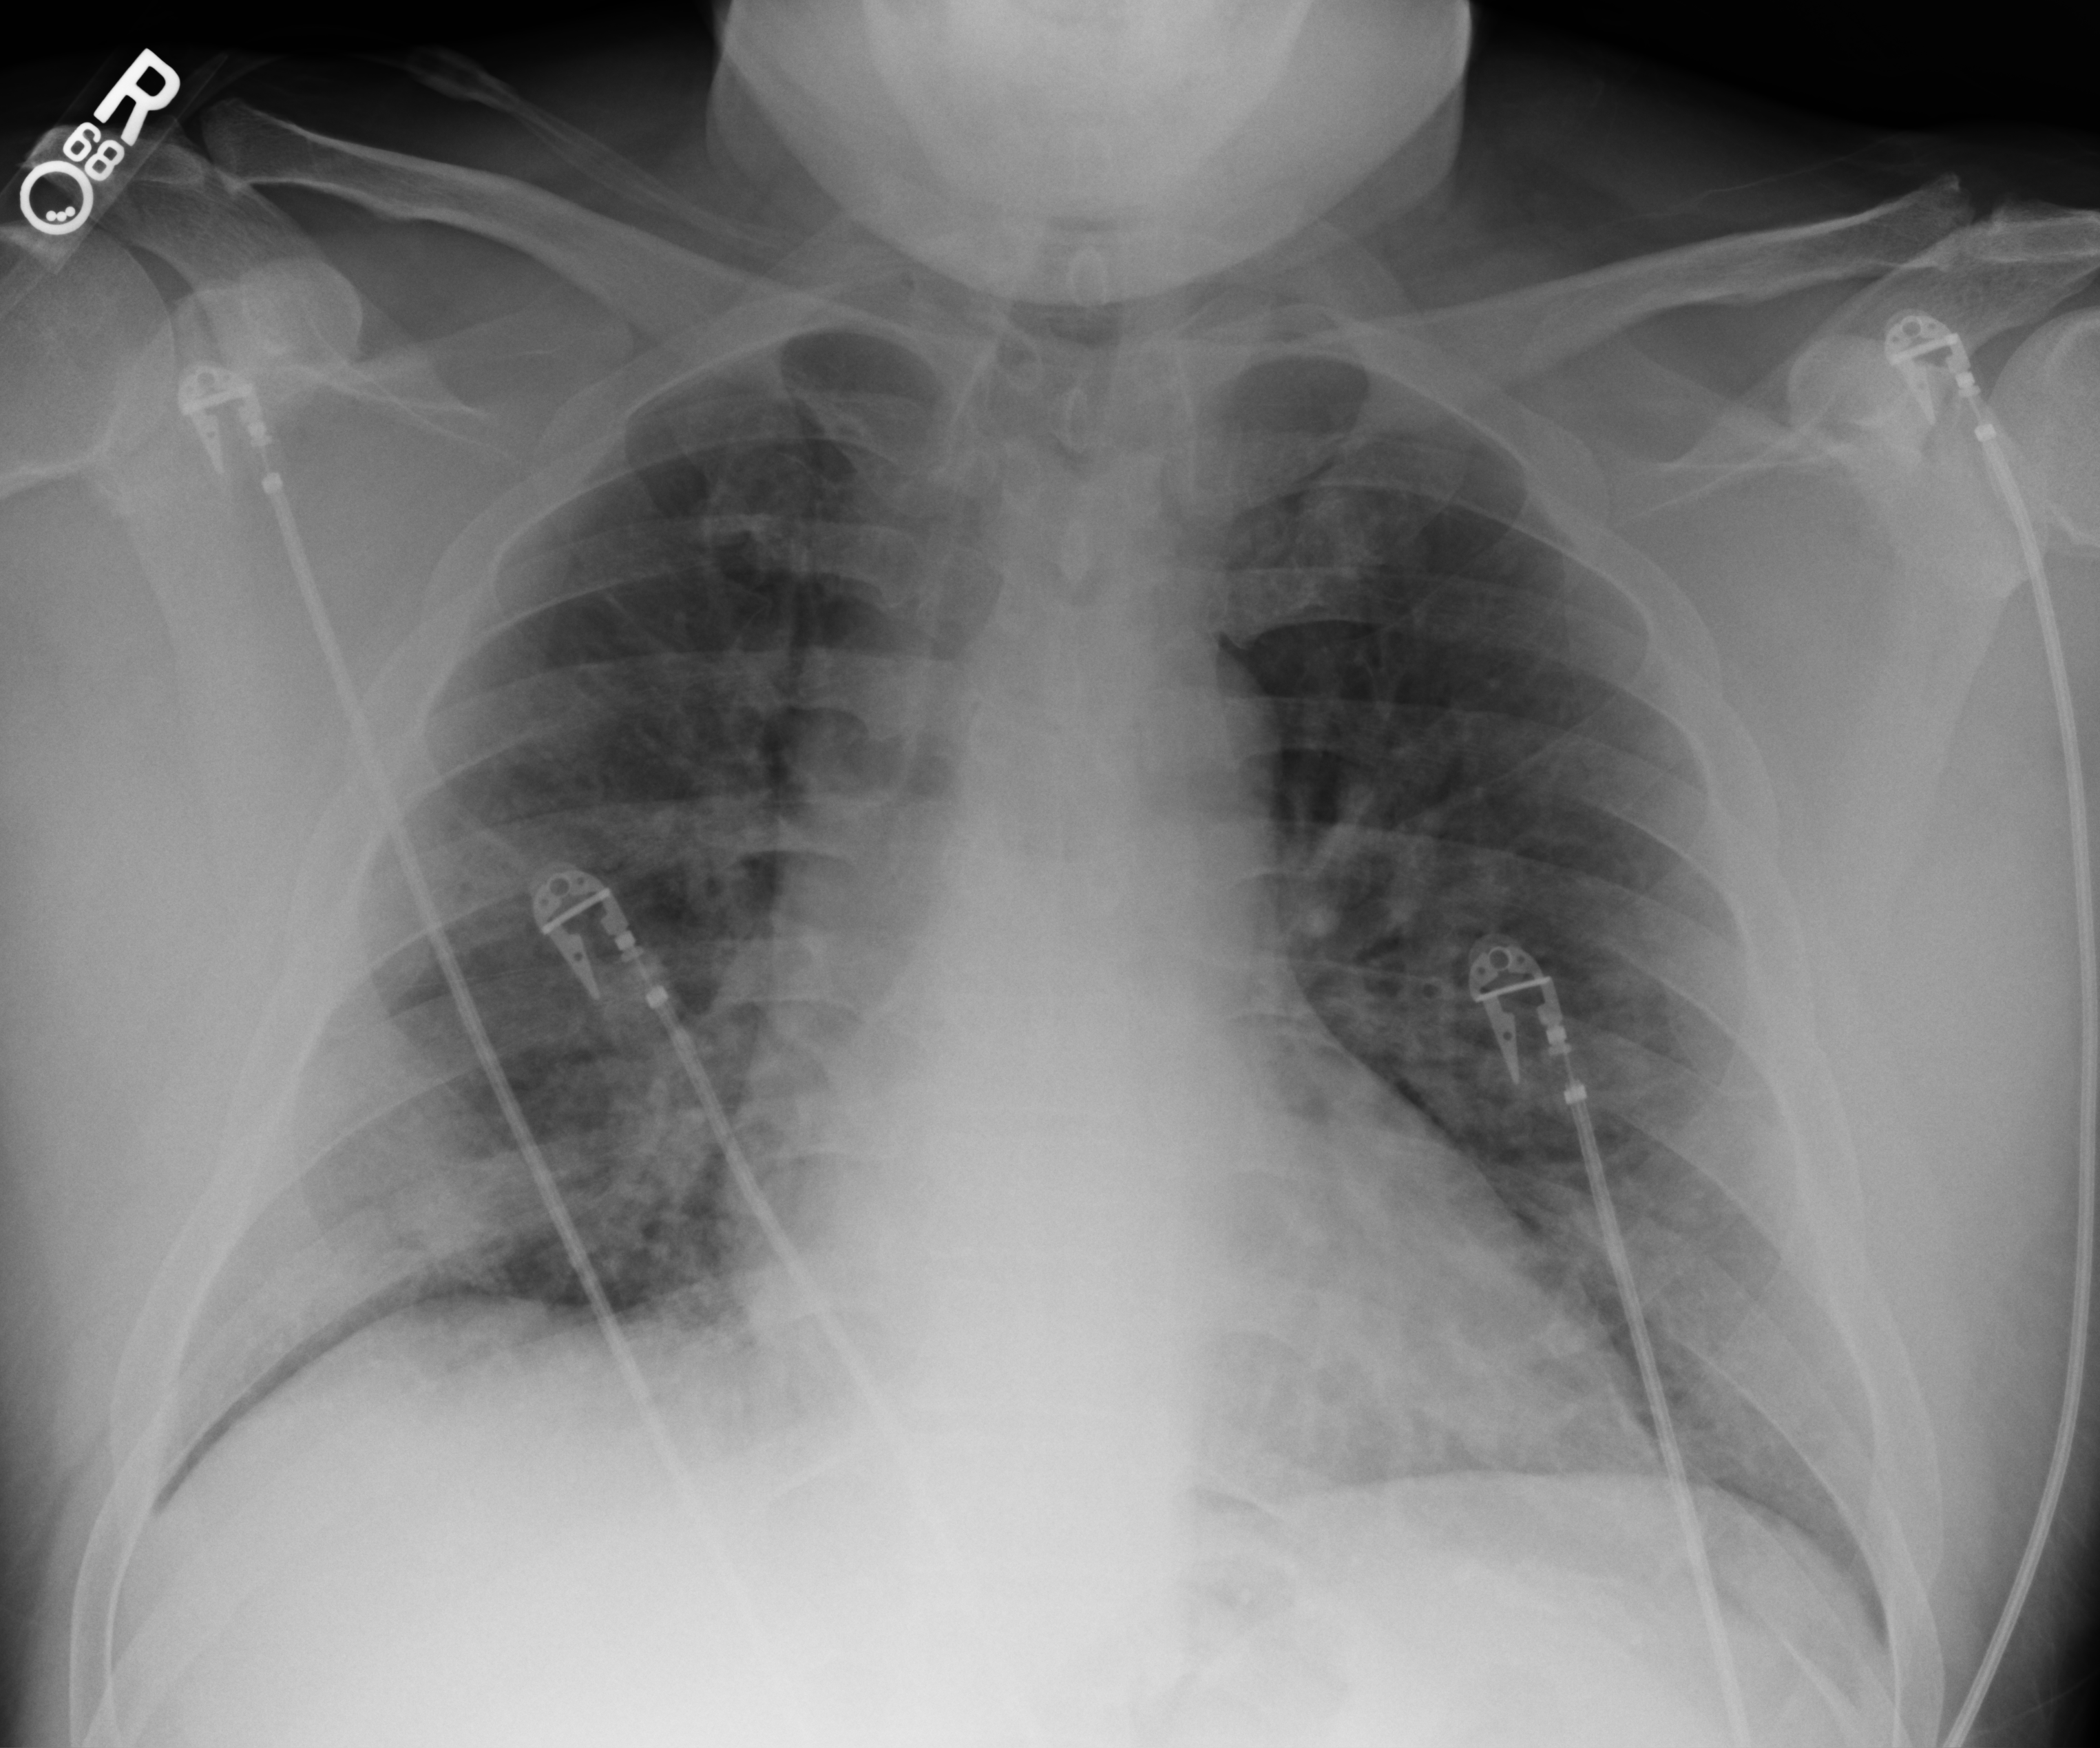
Portable chest radiograph; anteroposterior (AP) projection. Male patient hospitalised with COVID-19, age 18–59 years.
Admission-level facts for this patient (not findings on this image; timing relative to this image not recorded):
- admitted to intensive care during this hospital stay: no
- mechanically ventilated during this hospital stay: no
- length of hospital stay: 8 days